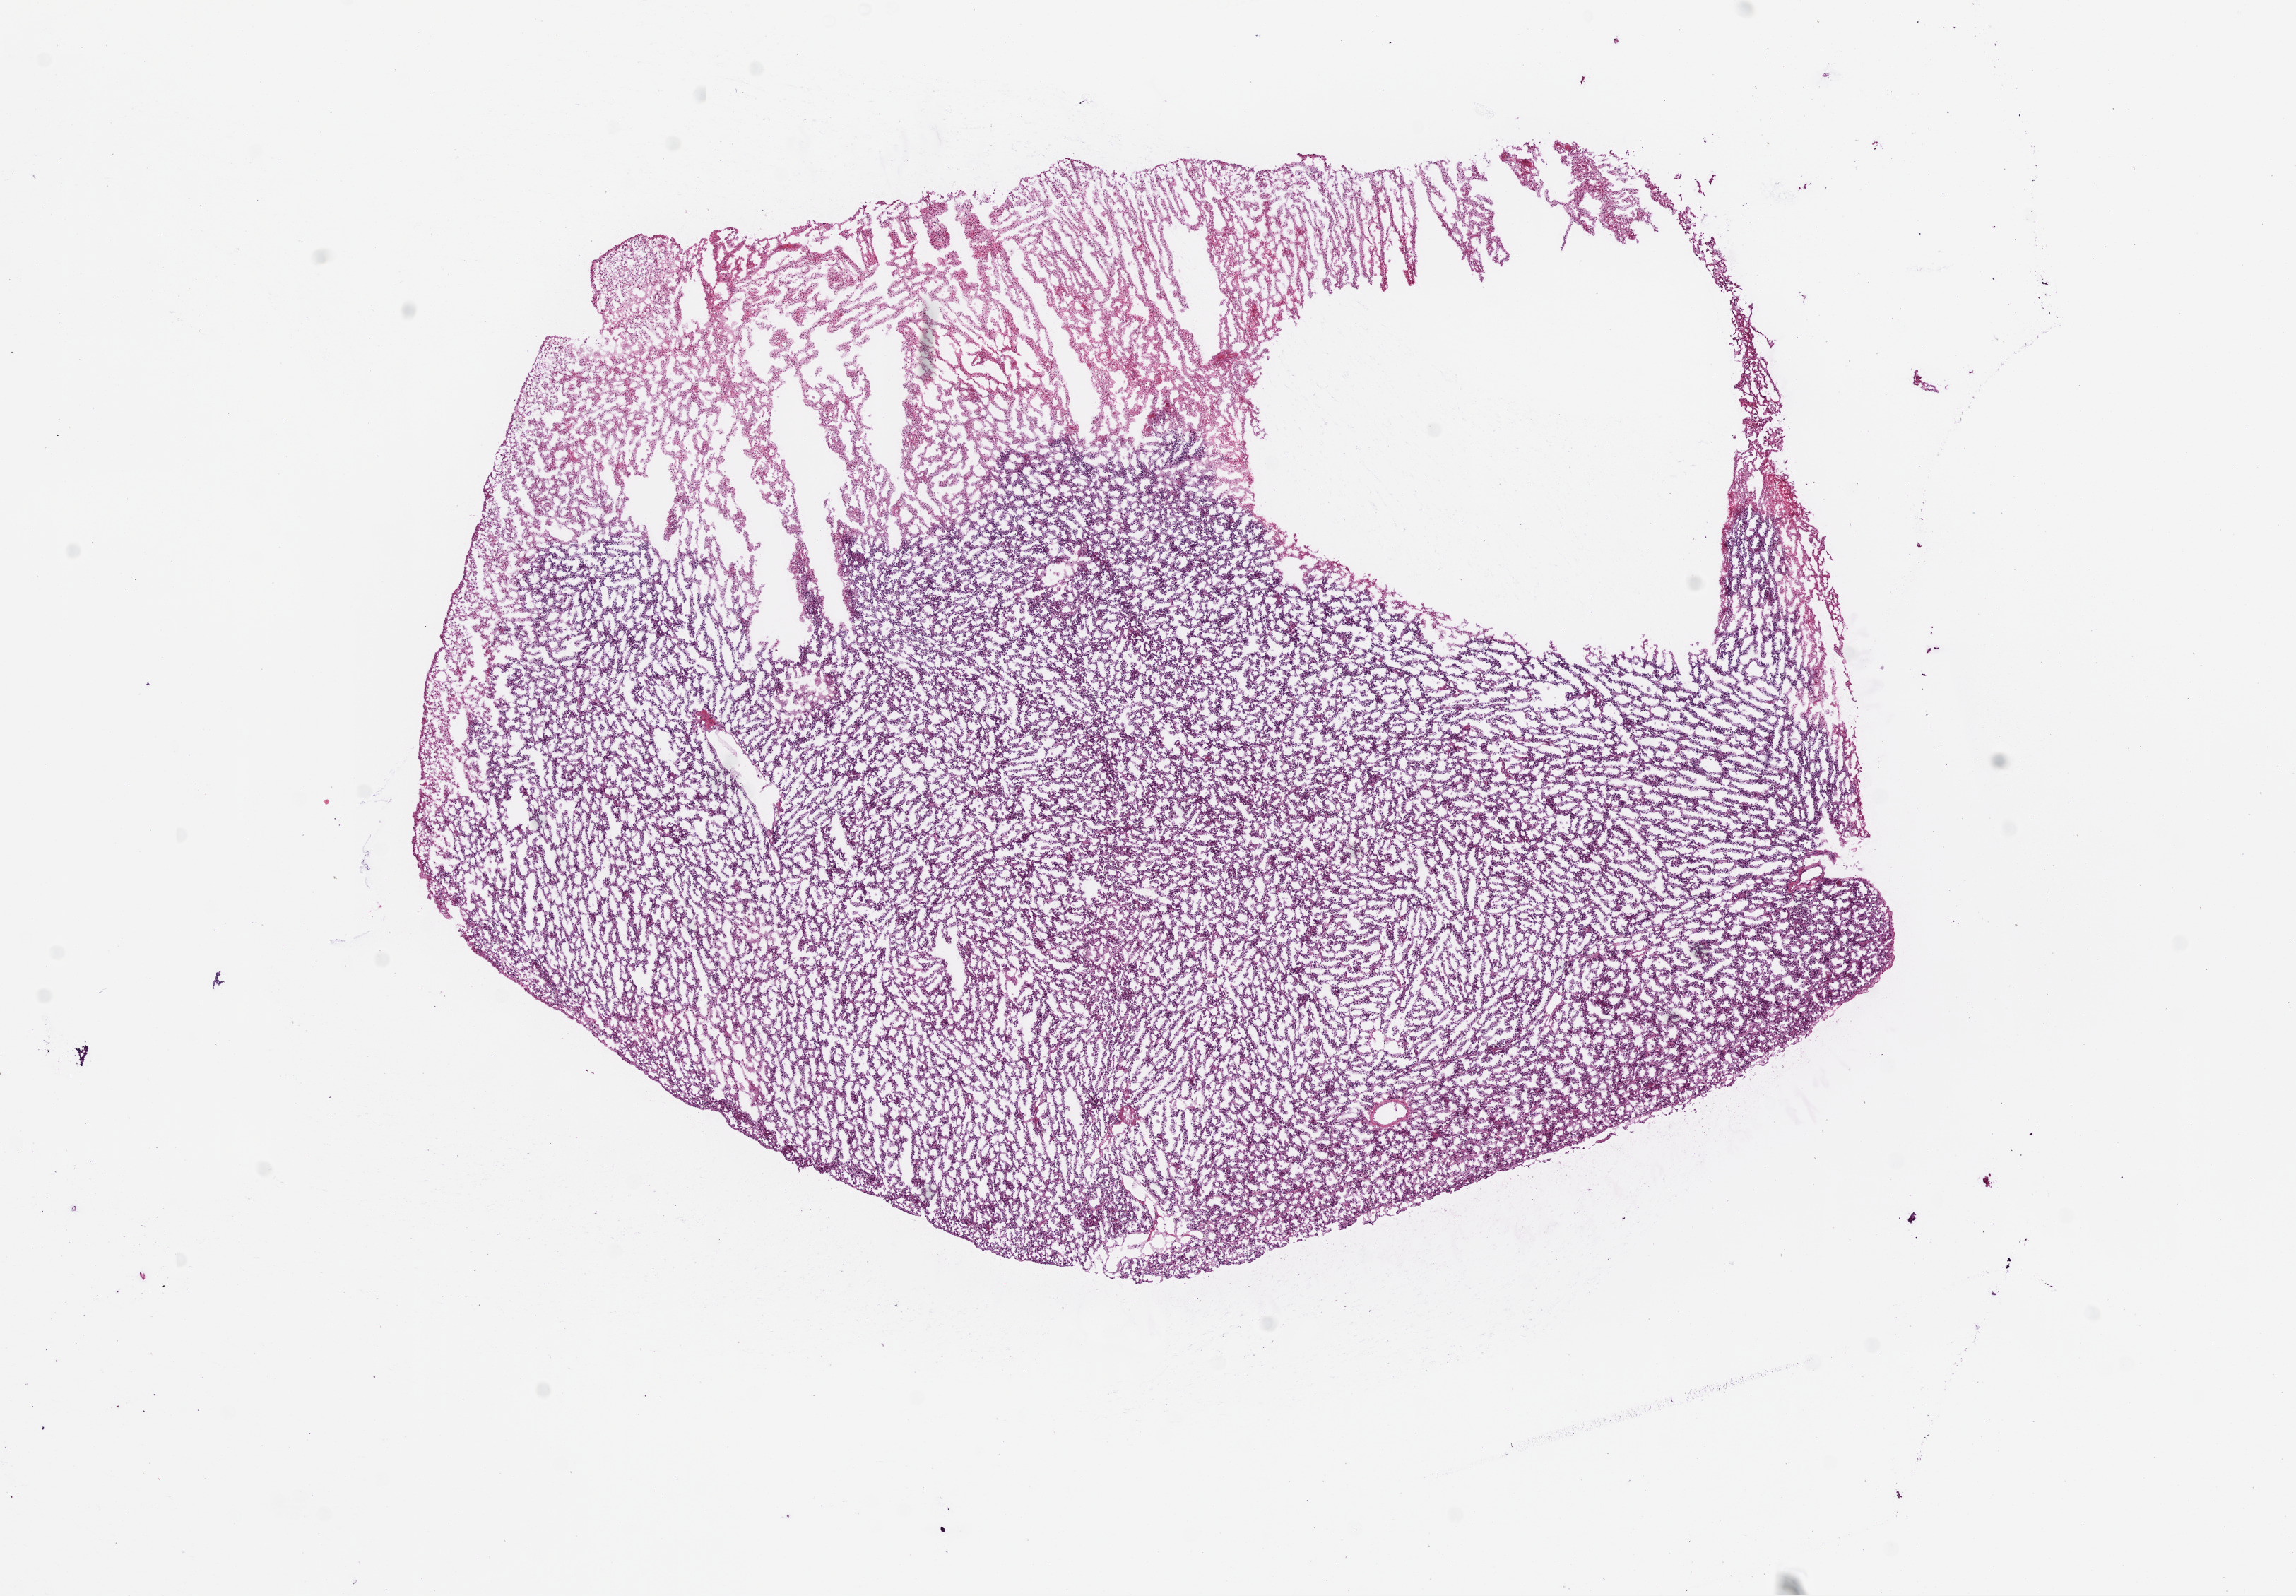
Whole-slide histology image, H&E — whole scanned area (about 13.0 x 9.1 mm) shown as a low-resolution overview. Frozen section from the bottom of the tissue portion. Primary tumour sample from the brain. Female, age 61 years at initial diagnosis. Composition of this section per pathologist review: tumour cells 75%, tumour nuclei 85%, normal cells 0%, stromal cells 0%, necrosis 25%.
Pathologic diagnosis: Glioblastoma.